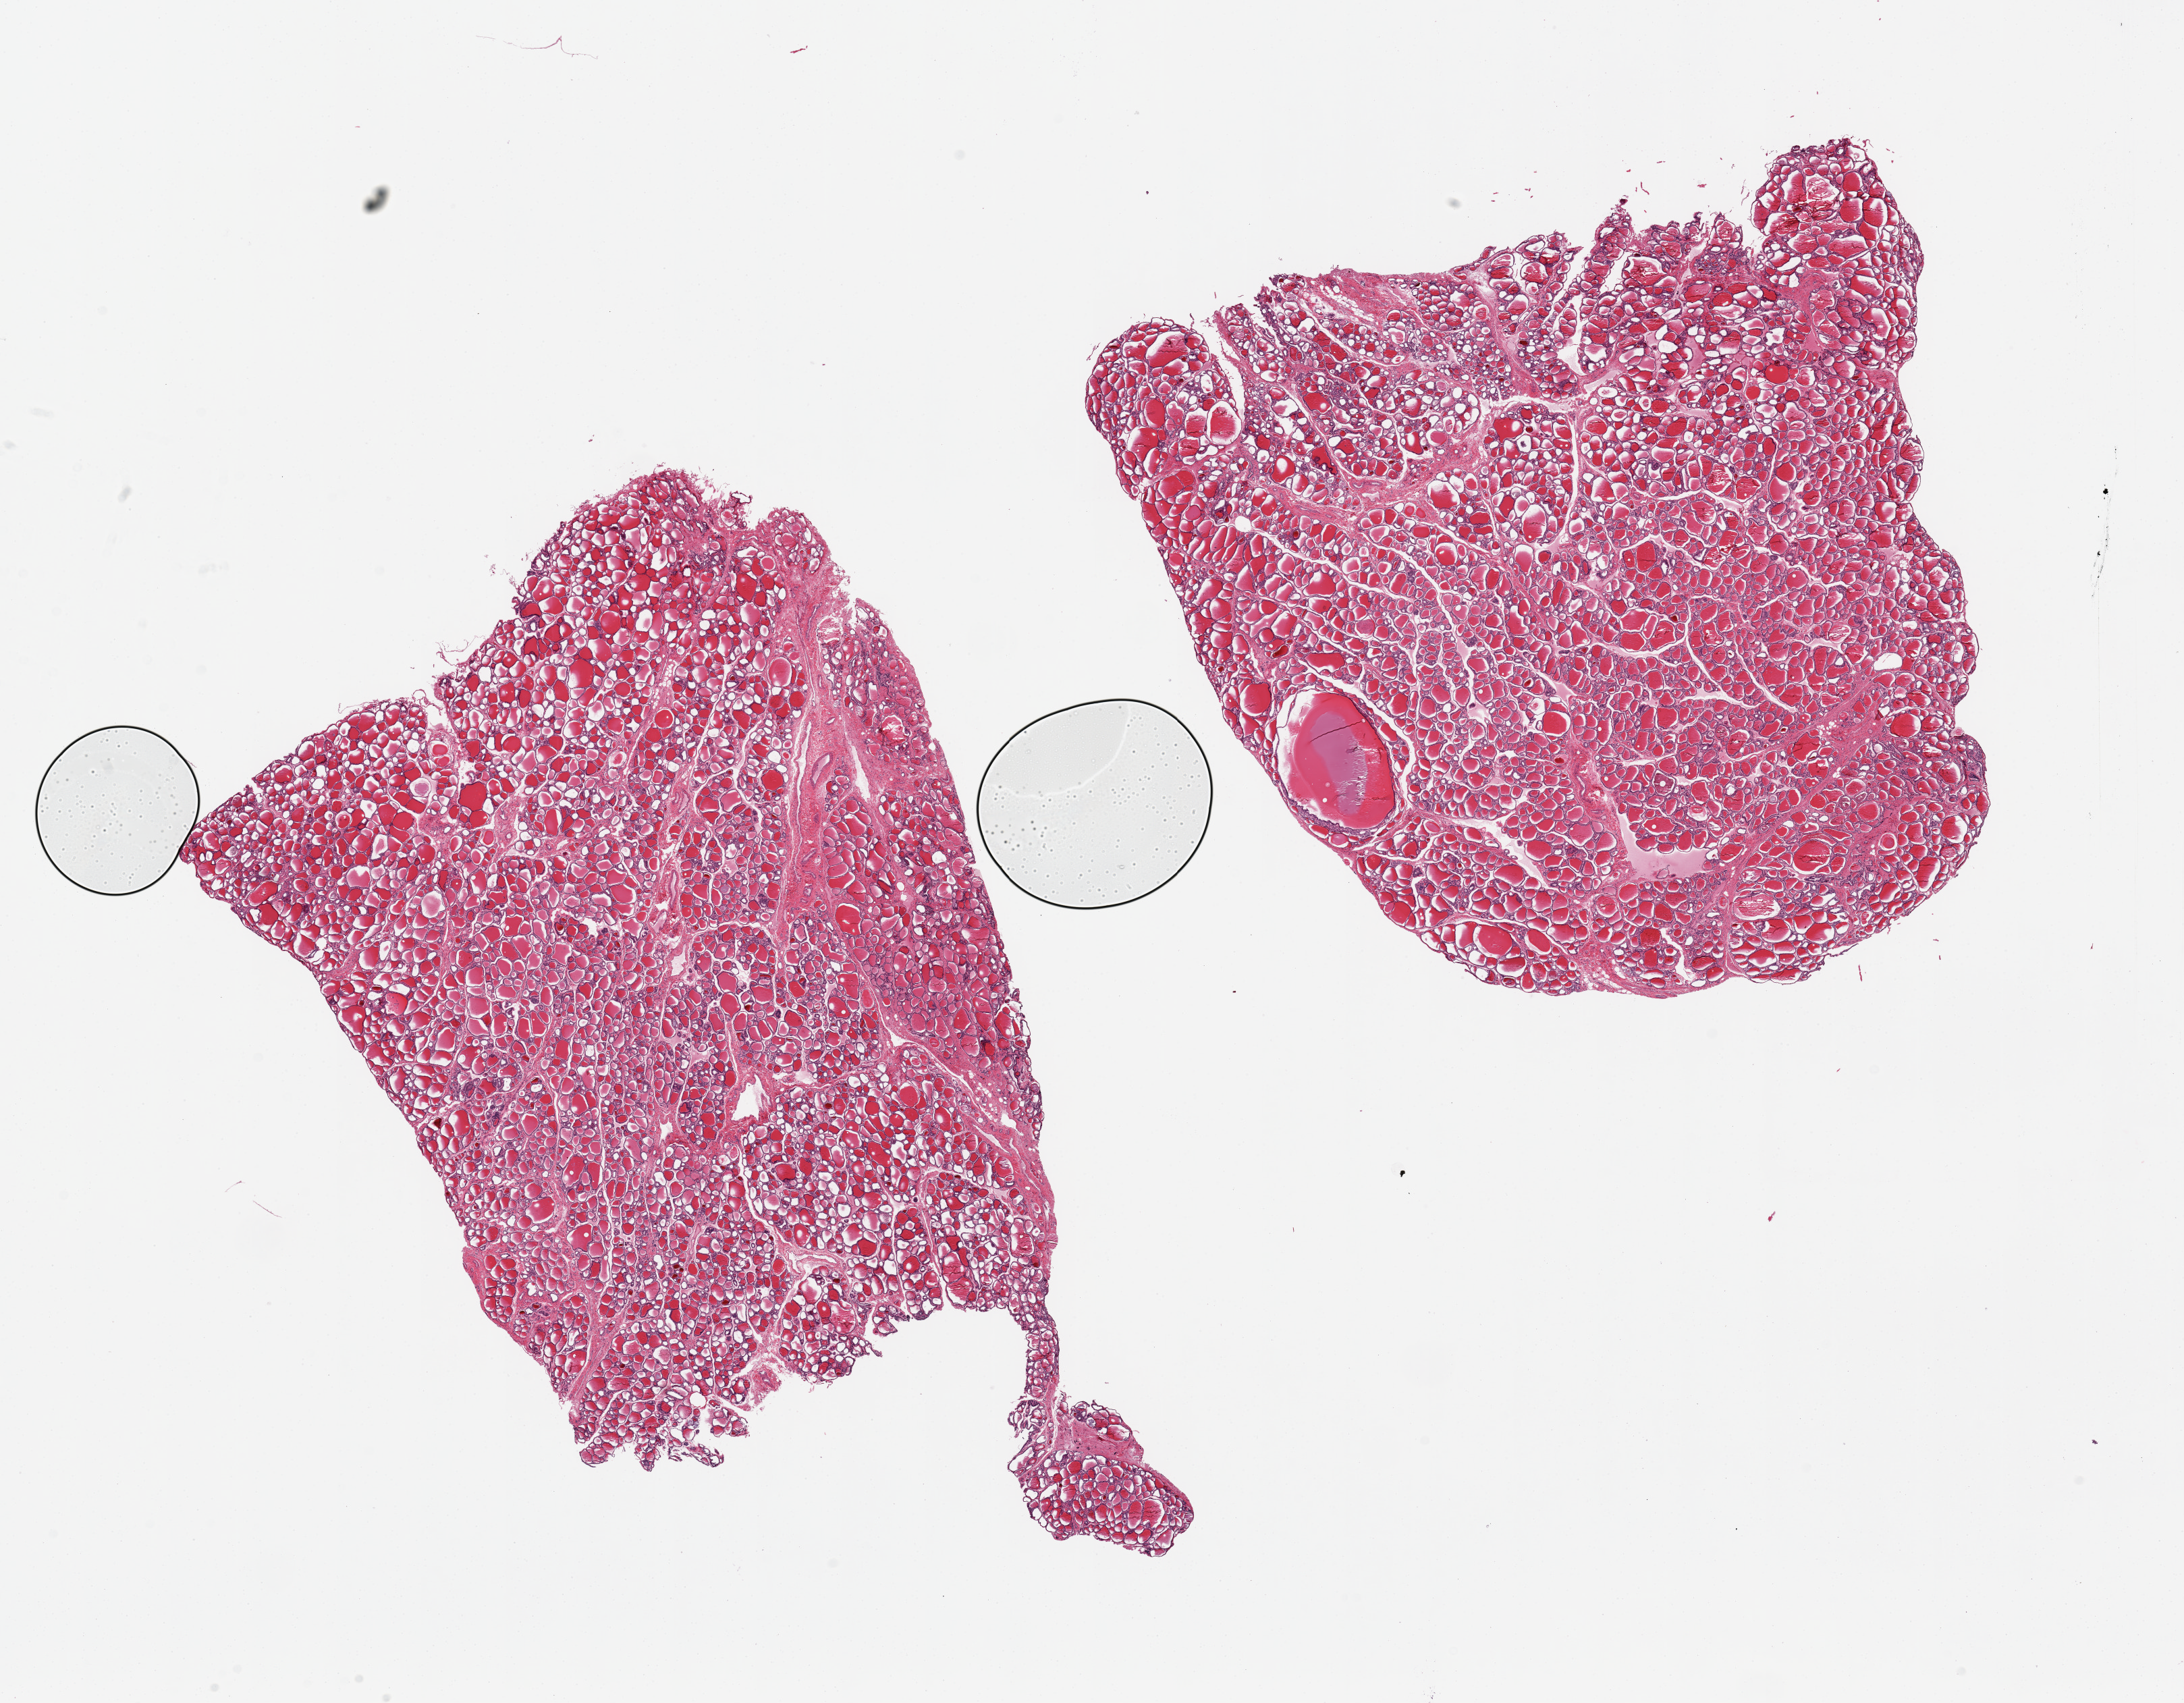
Haematoxylin and eosin whole-slide image, brightfield — low-resolution overview of the scanned area, about 25.6 x 20.0 mm (from a 20x scan). PAXgene-fixed, paraffin-embedded tissue. Section of thyroid (target tissue). Donor tissue sample.
Pathologist's review note for this sample: 2 pieces. 14x9 & 10x10mm.